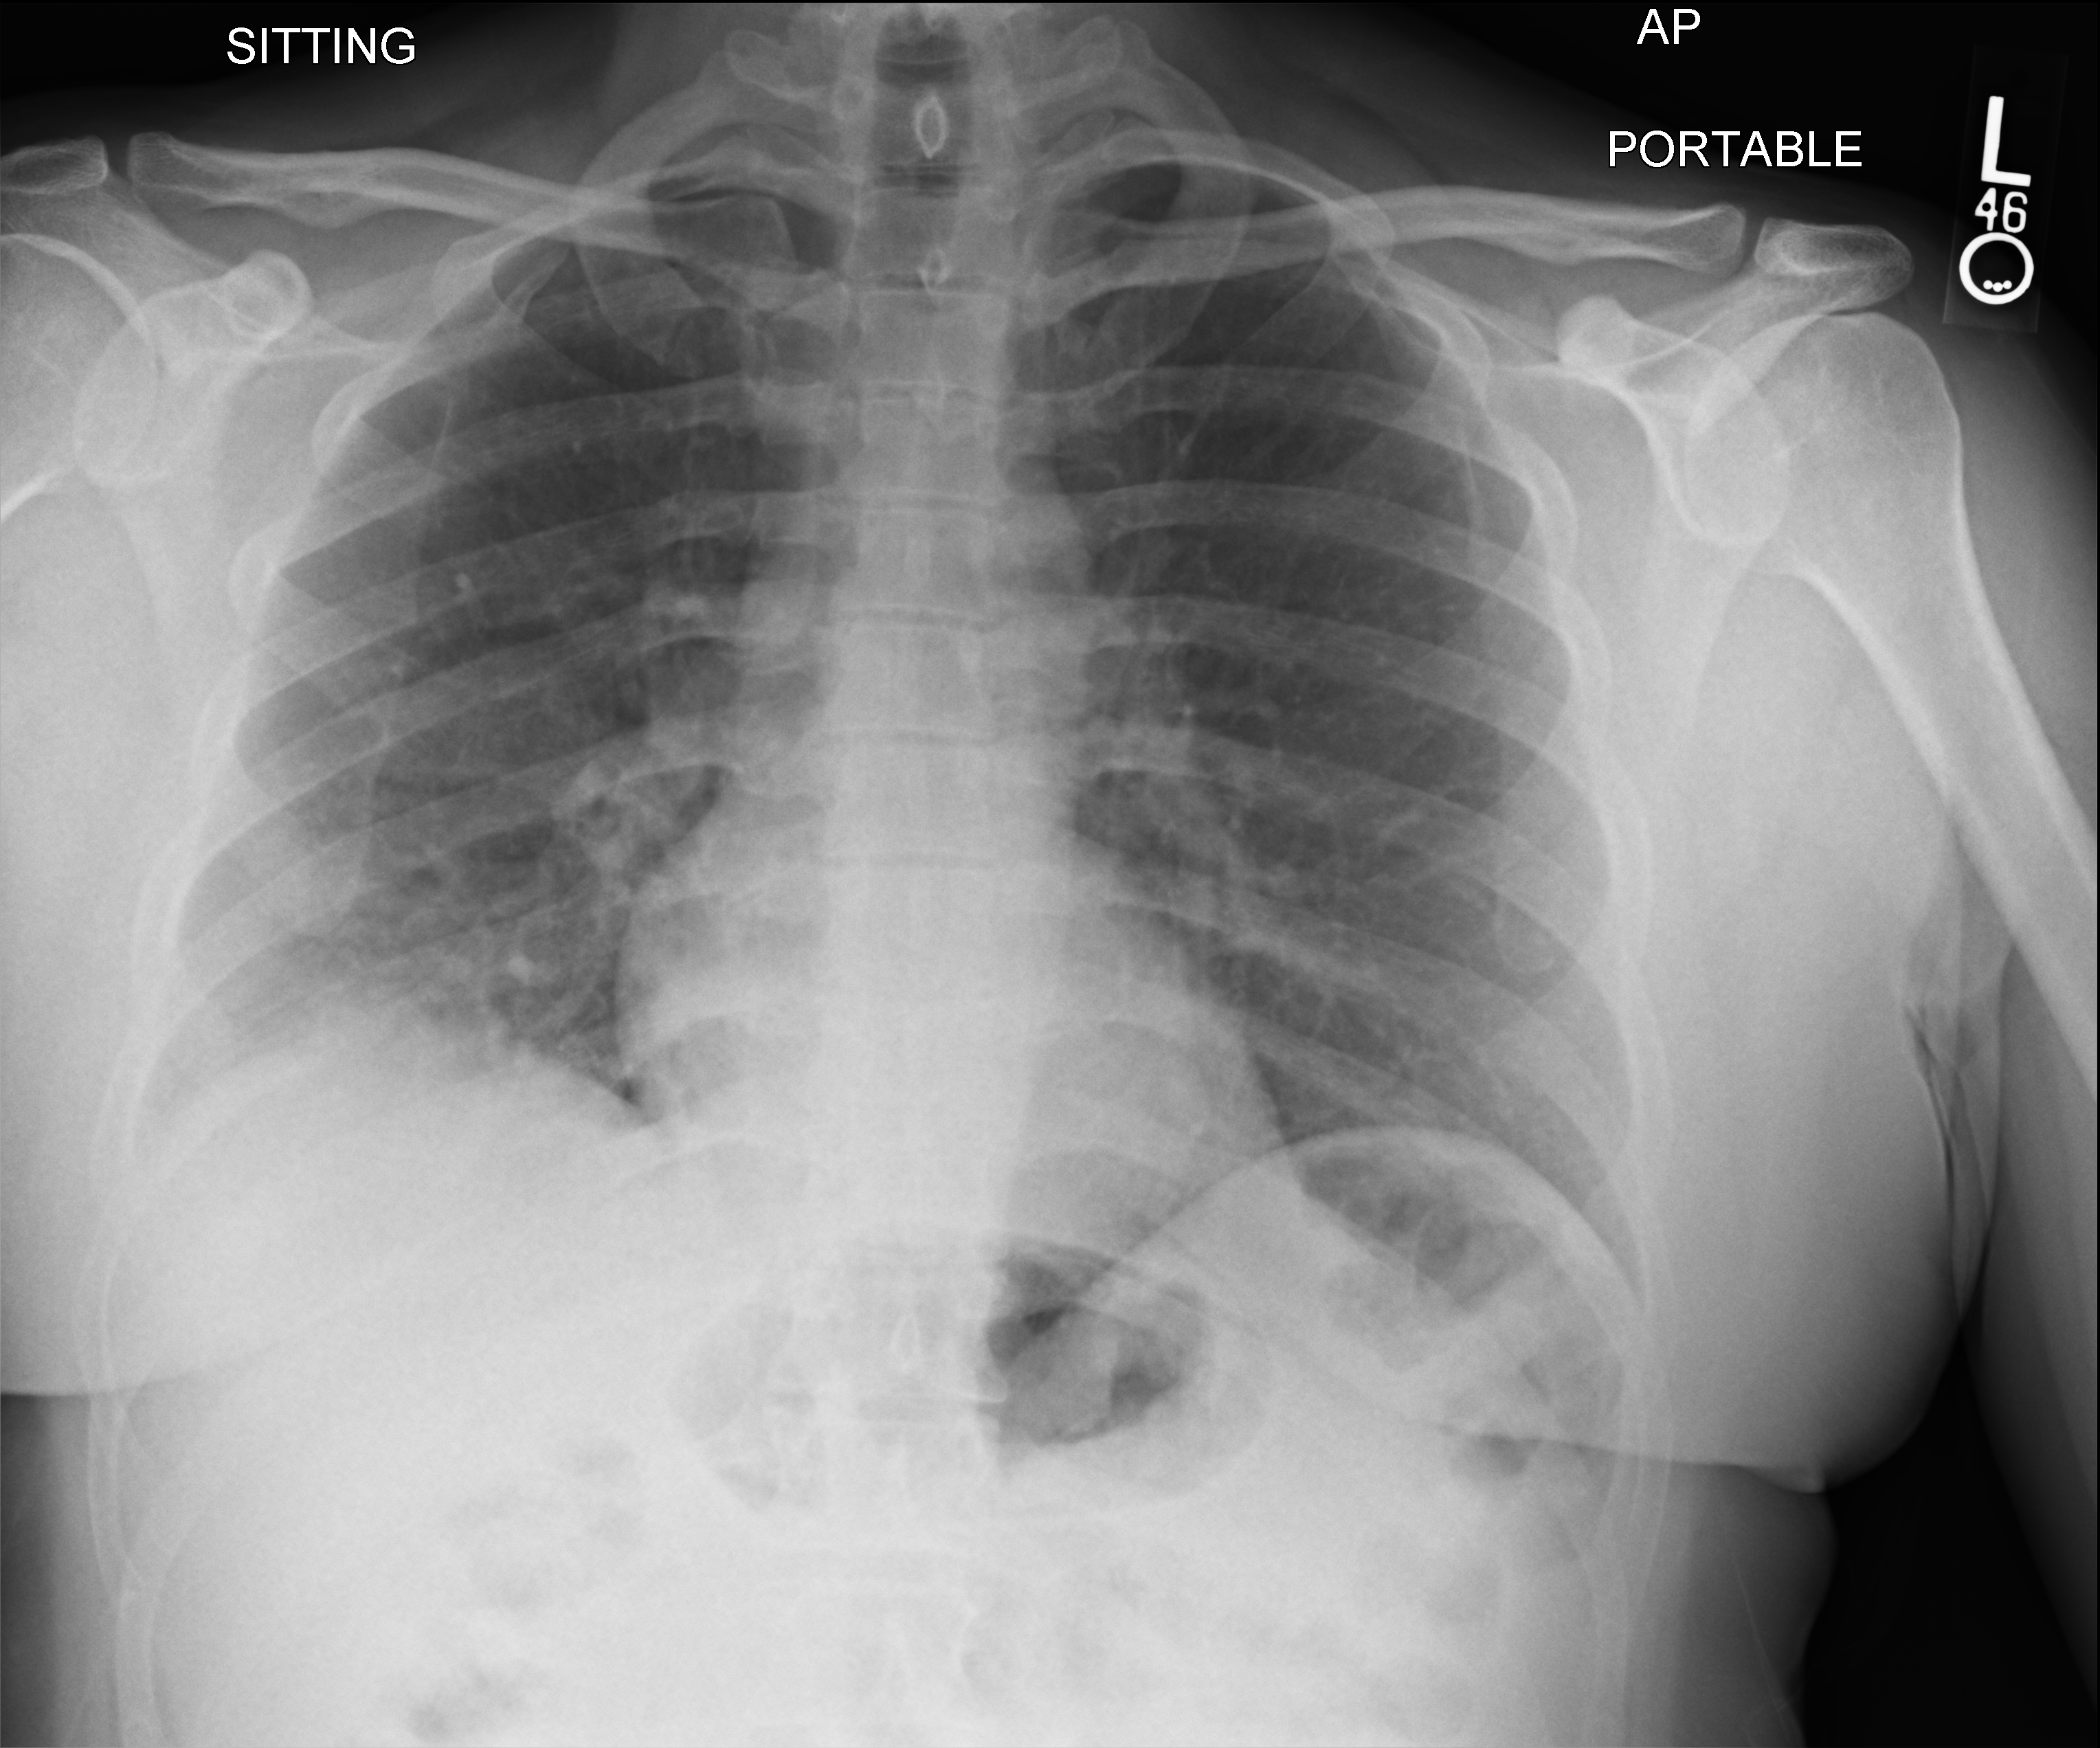
Chest X-ray (portable). Patient hospitalised with COVID-19; male, aged 18–59 years.
From the hospital-stay record, not from the radiograph (when in the stay this image was taken is not recorded): length of hospital stay: 1 day.